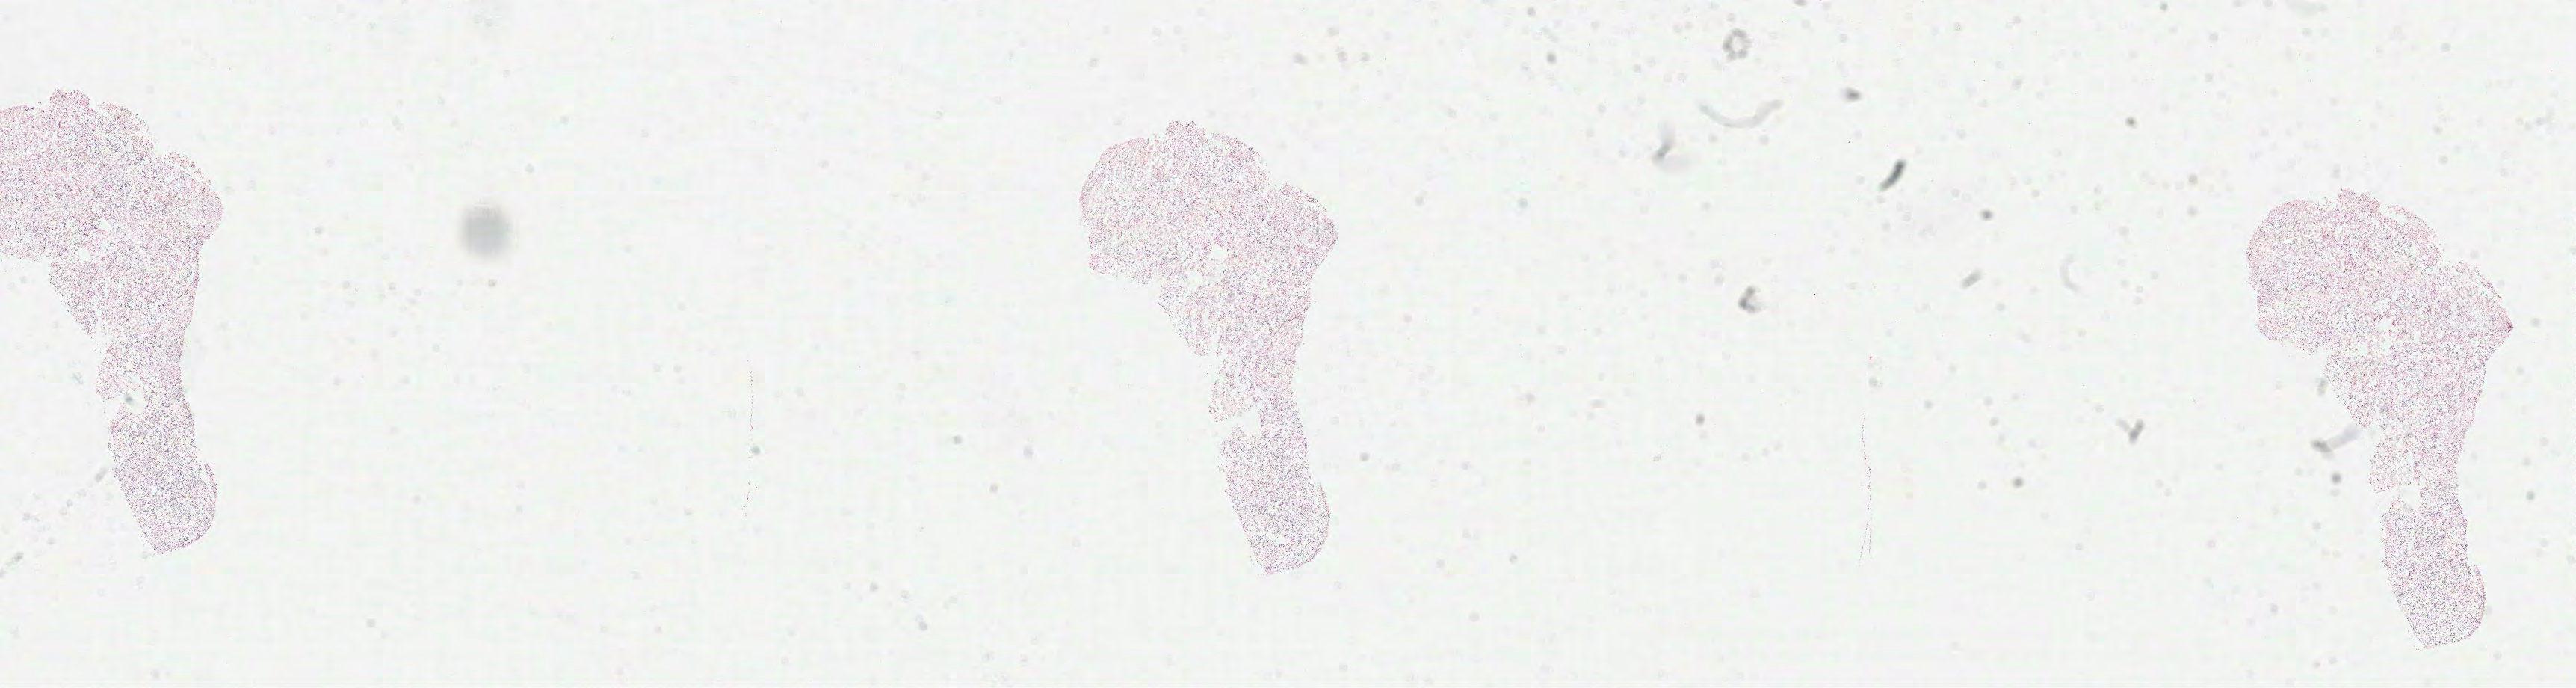
Digitized H&E-stained tissue section (whole slide), shown as a low-resolution overview of the whole scanned area (about 27.8 x 7.4 mm, acquisition: 40x scan). Formalin-fixed paraffin-embedded (FFPE) diagnostic section. Primary tumour sample from the brain. Female patient; age at initial diagnosis 83 years.
- pathologic diagnosis: Glioblastoma